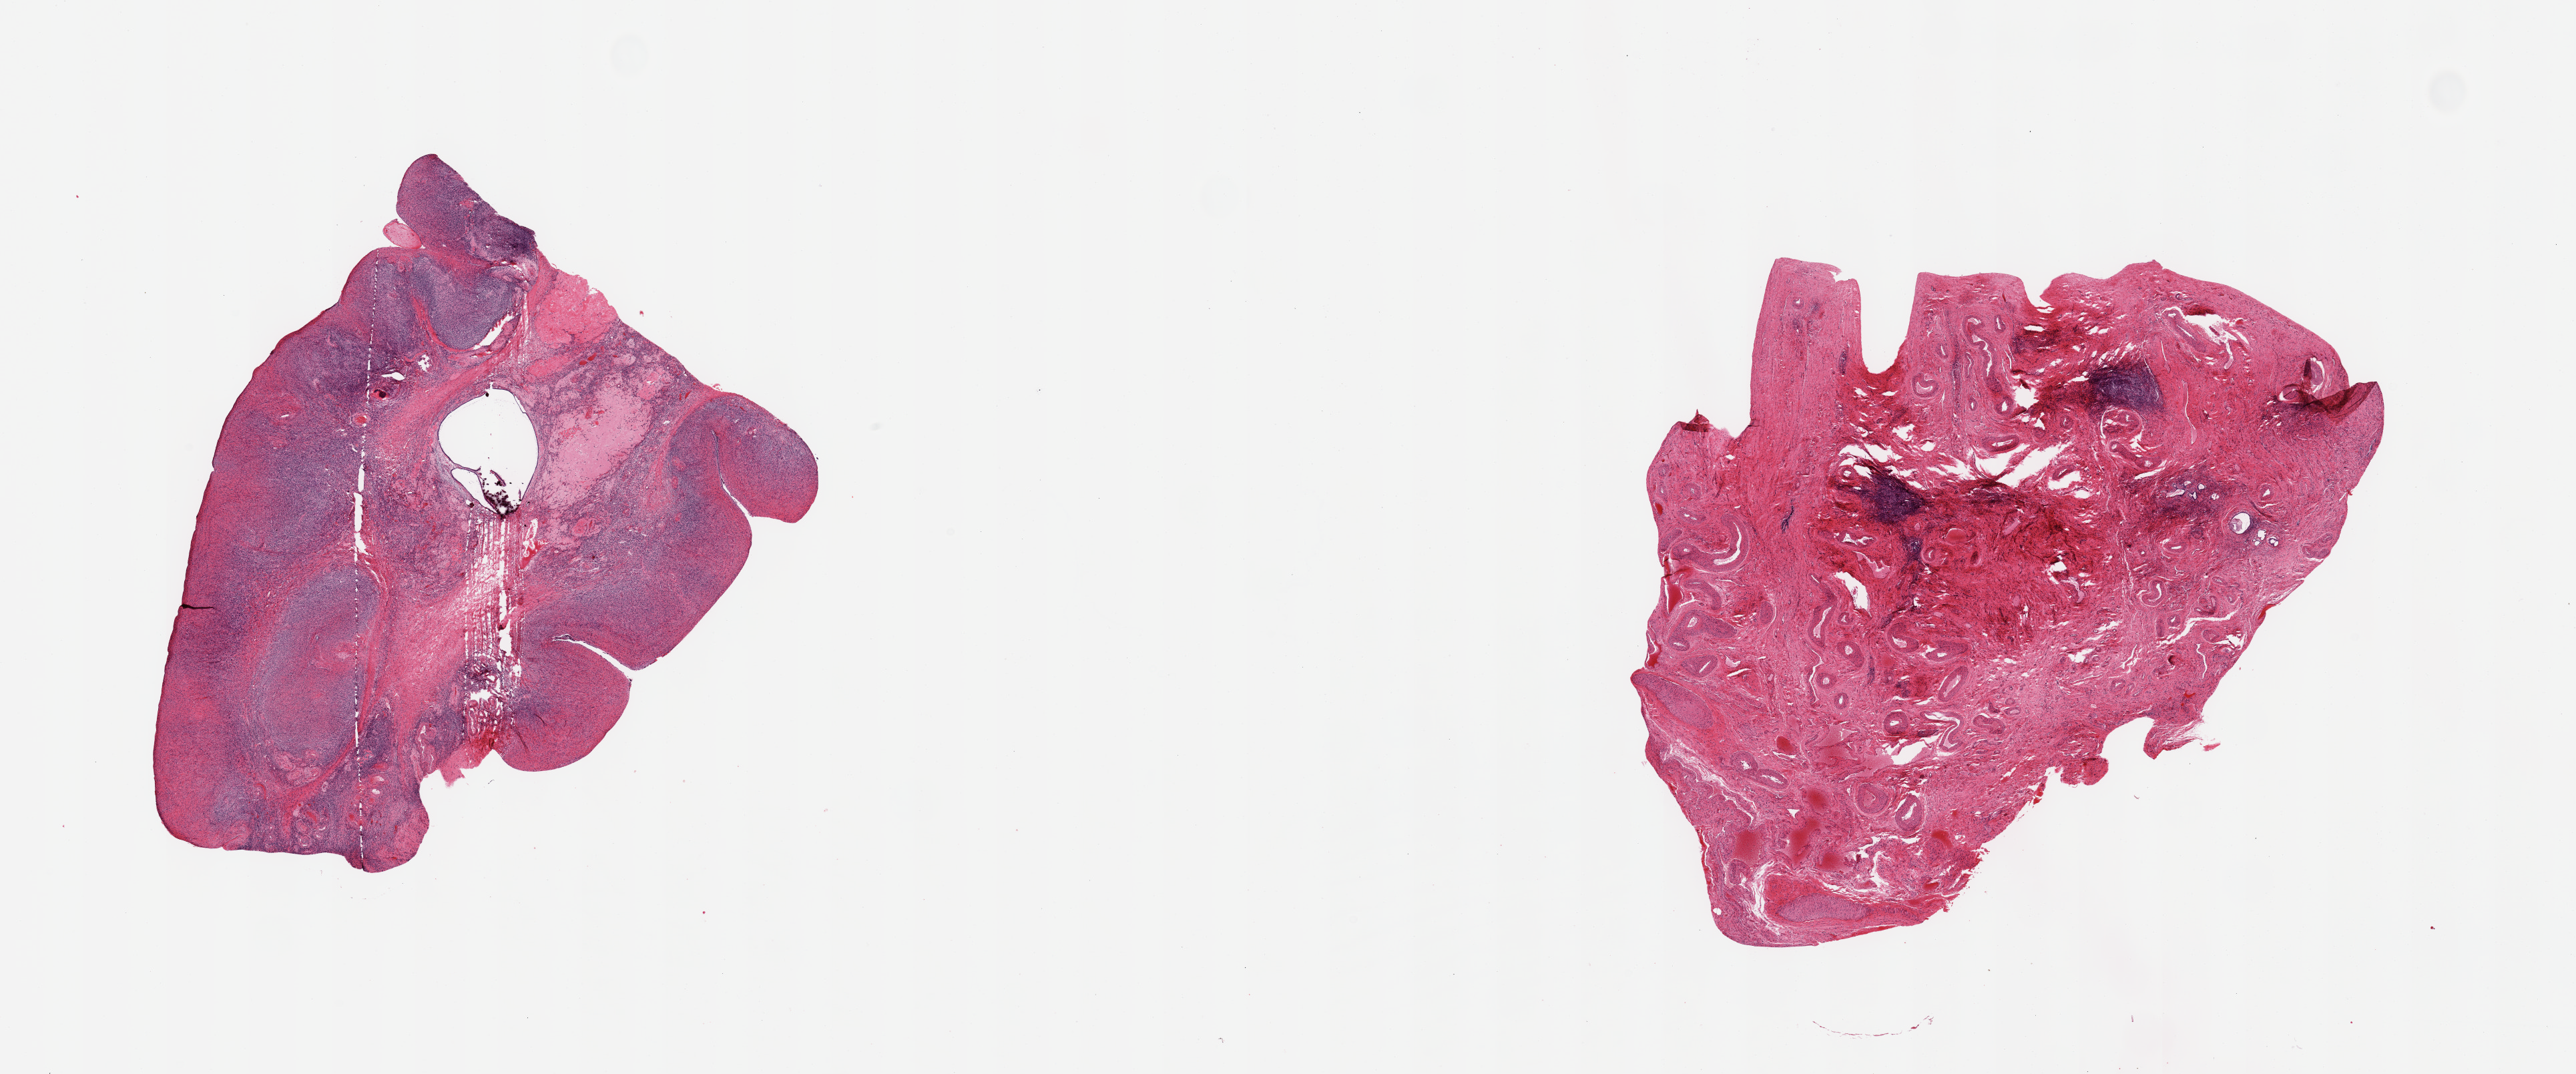
Whole-slide image, hematoxylin and eosin (H&E) stain, shown as a low-resolution overview of the whole scanned area (about 30.5 x 12.7 mm, acquisition: 20x scan), PAXgene-fixed, paraffin-embedded tissue, target tissue: ovary, tissue donor sample. Female donor.
Pathologist's review note for this sample: 2 pieces; 1 piece is ovarian stroma with corpora albicantia/fibrosa and cyst with focal calcification, 2nd is predominantly vessels.